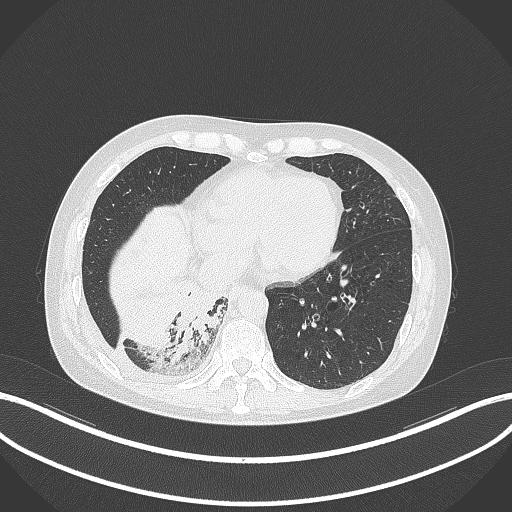
Chest CT, one axial slice; position 89 of 329 along the scan axis; reconstruction kernel B70f; 120 kVp; lung window (W 1500 / L -600 HU); 1 mm slice thickness; 512 × 512 image matrix. Patient: female, 63 years. Case-level facts recorded for this patient, not image findings: clinical TNM (as recorded): T1c N0 M0.
Annotated regions visible in this slice (rectangle marked by the reading radiologist):
- lung tumour (recorded histology: adenocarcinoma): bounding box [x1, y1, x2, y2] px = [170, 286, 229, 362]